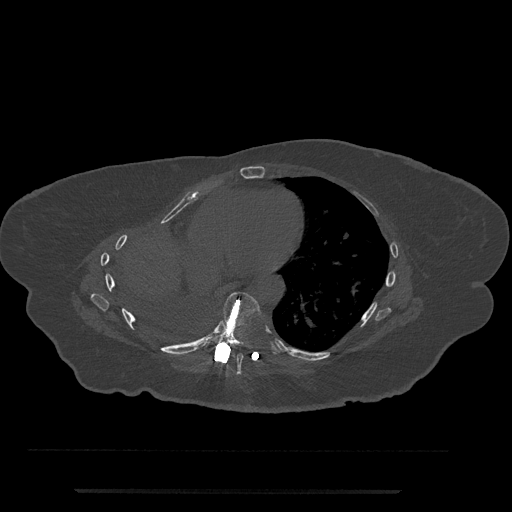
CT including the spine, one axial slice; slice 405 of 797 in the series (ordered by position); 120 kVp; bone window (W 1800 / L 400 HU); 0.5 mm slice thickness; 512 × 512 image matrix, field of view 440 × 440 mm. Female patient, age 51 years. From the clinical record (not read from this slice): primary cancer: neuro; vertebrae with lytic lesions (as recorded): T8.
Outlined on this slice (semi-automatically segmented with operator editing):
- T7 vertebra: bounding box <233,353,243,375> (left, top, right, bottom; pixels)
- T8 vertebra: <204,292,261,351>